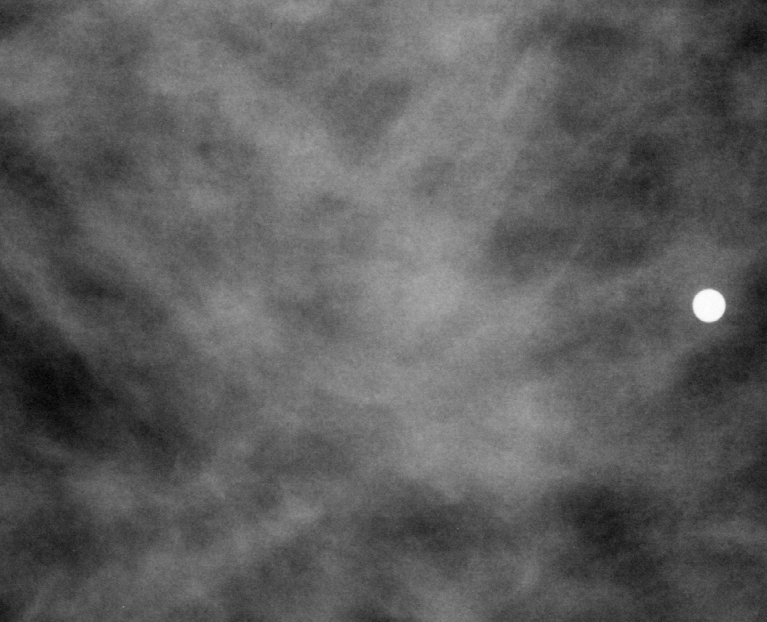
Cropped region of a digitized screen-film mammogram centred on a radiologist-marked abnormality; left breast; CC view.
Mass, shape architectural distortion, margins ill defined; BI-RADS assessment category 4; pathology (as recorded): malignant.